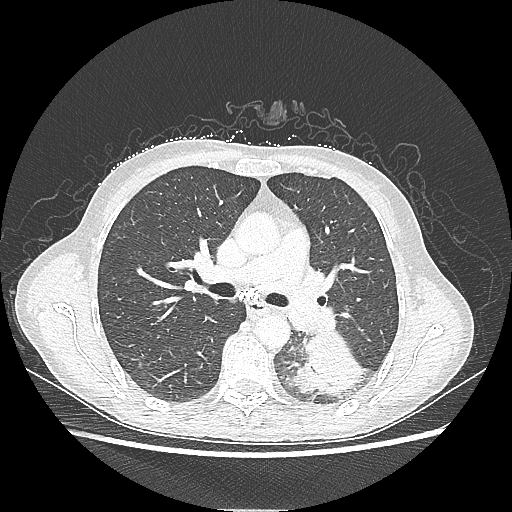
Chest CT, one axial slice. Slice 133 of 220 in the series (ordered by position). Reconstruction kernel LUNG. Lung window (W 1500 / L -600 HU). 1.25 mm slice thickness. 512 × 512 image matrix, field of view 360 × 360 mm. Patient: female, 53 years. From the clinical record (not read from this slice): clinical TNM (as recorded): T3 N0 M0.
Annotated regions visible in this slice (rectangle marked by the reading radiologist):
- lung tumour (recorded histology: adenocarcinoma): box from (x=290, y=332) to (x=366, y=398) px